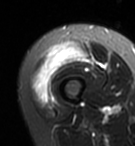
MRI of an extremity soft-tissue mass, one axial slice. Slice 15 of 95 in the series (ordered by position). T2-weighted fat-saturated. MR volume resampled by the dataset authors to the PET/CT grid (not the native acquisition matrix). 135 × 146 image matrix. Female patient. Case-level facts recorded for this patient, not image findings: histological type: pleiomorphic undifferentiated sarcoma; grade: high; site of the primary tumour: right quadricep.
Annotated regions visible in this slice (expert contour drawn on MRI and transferred to this co-registered scan by the dataset authors):
- gross tumour volume including surrounding oedema: bounding box <32,43,88,105> (left, top, right, bottom; pixels)